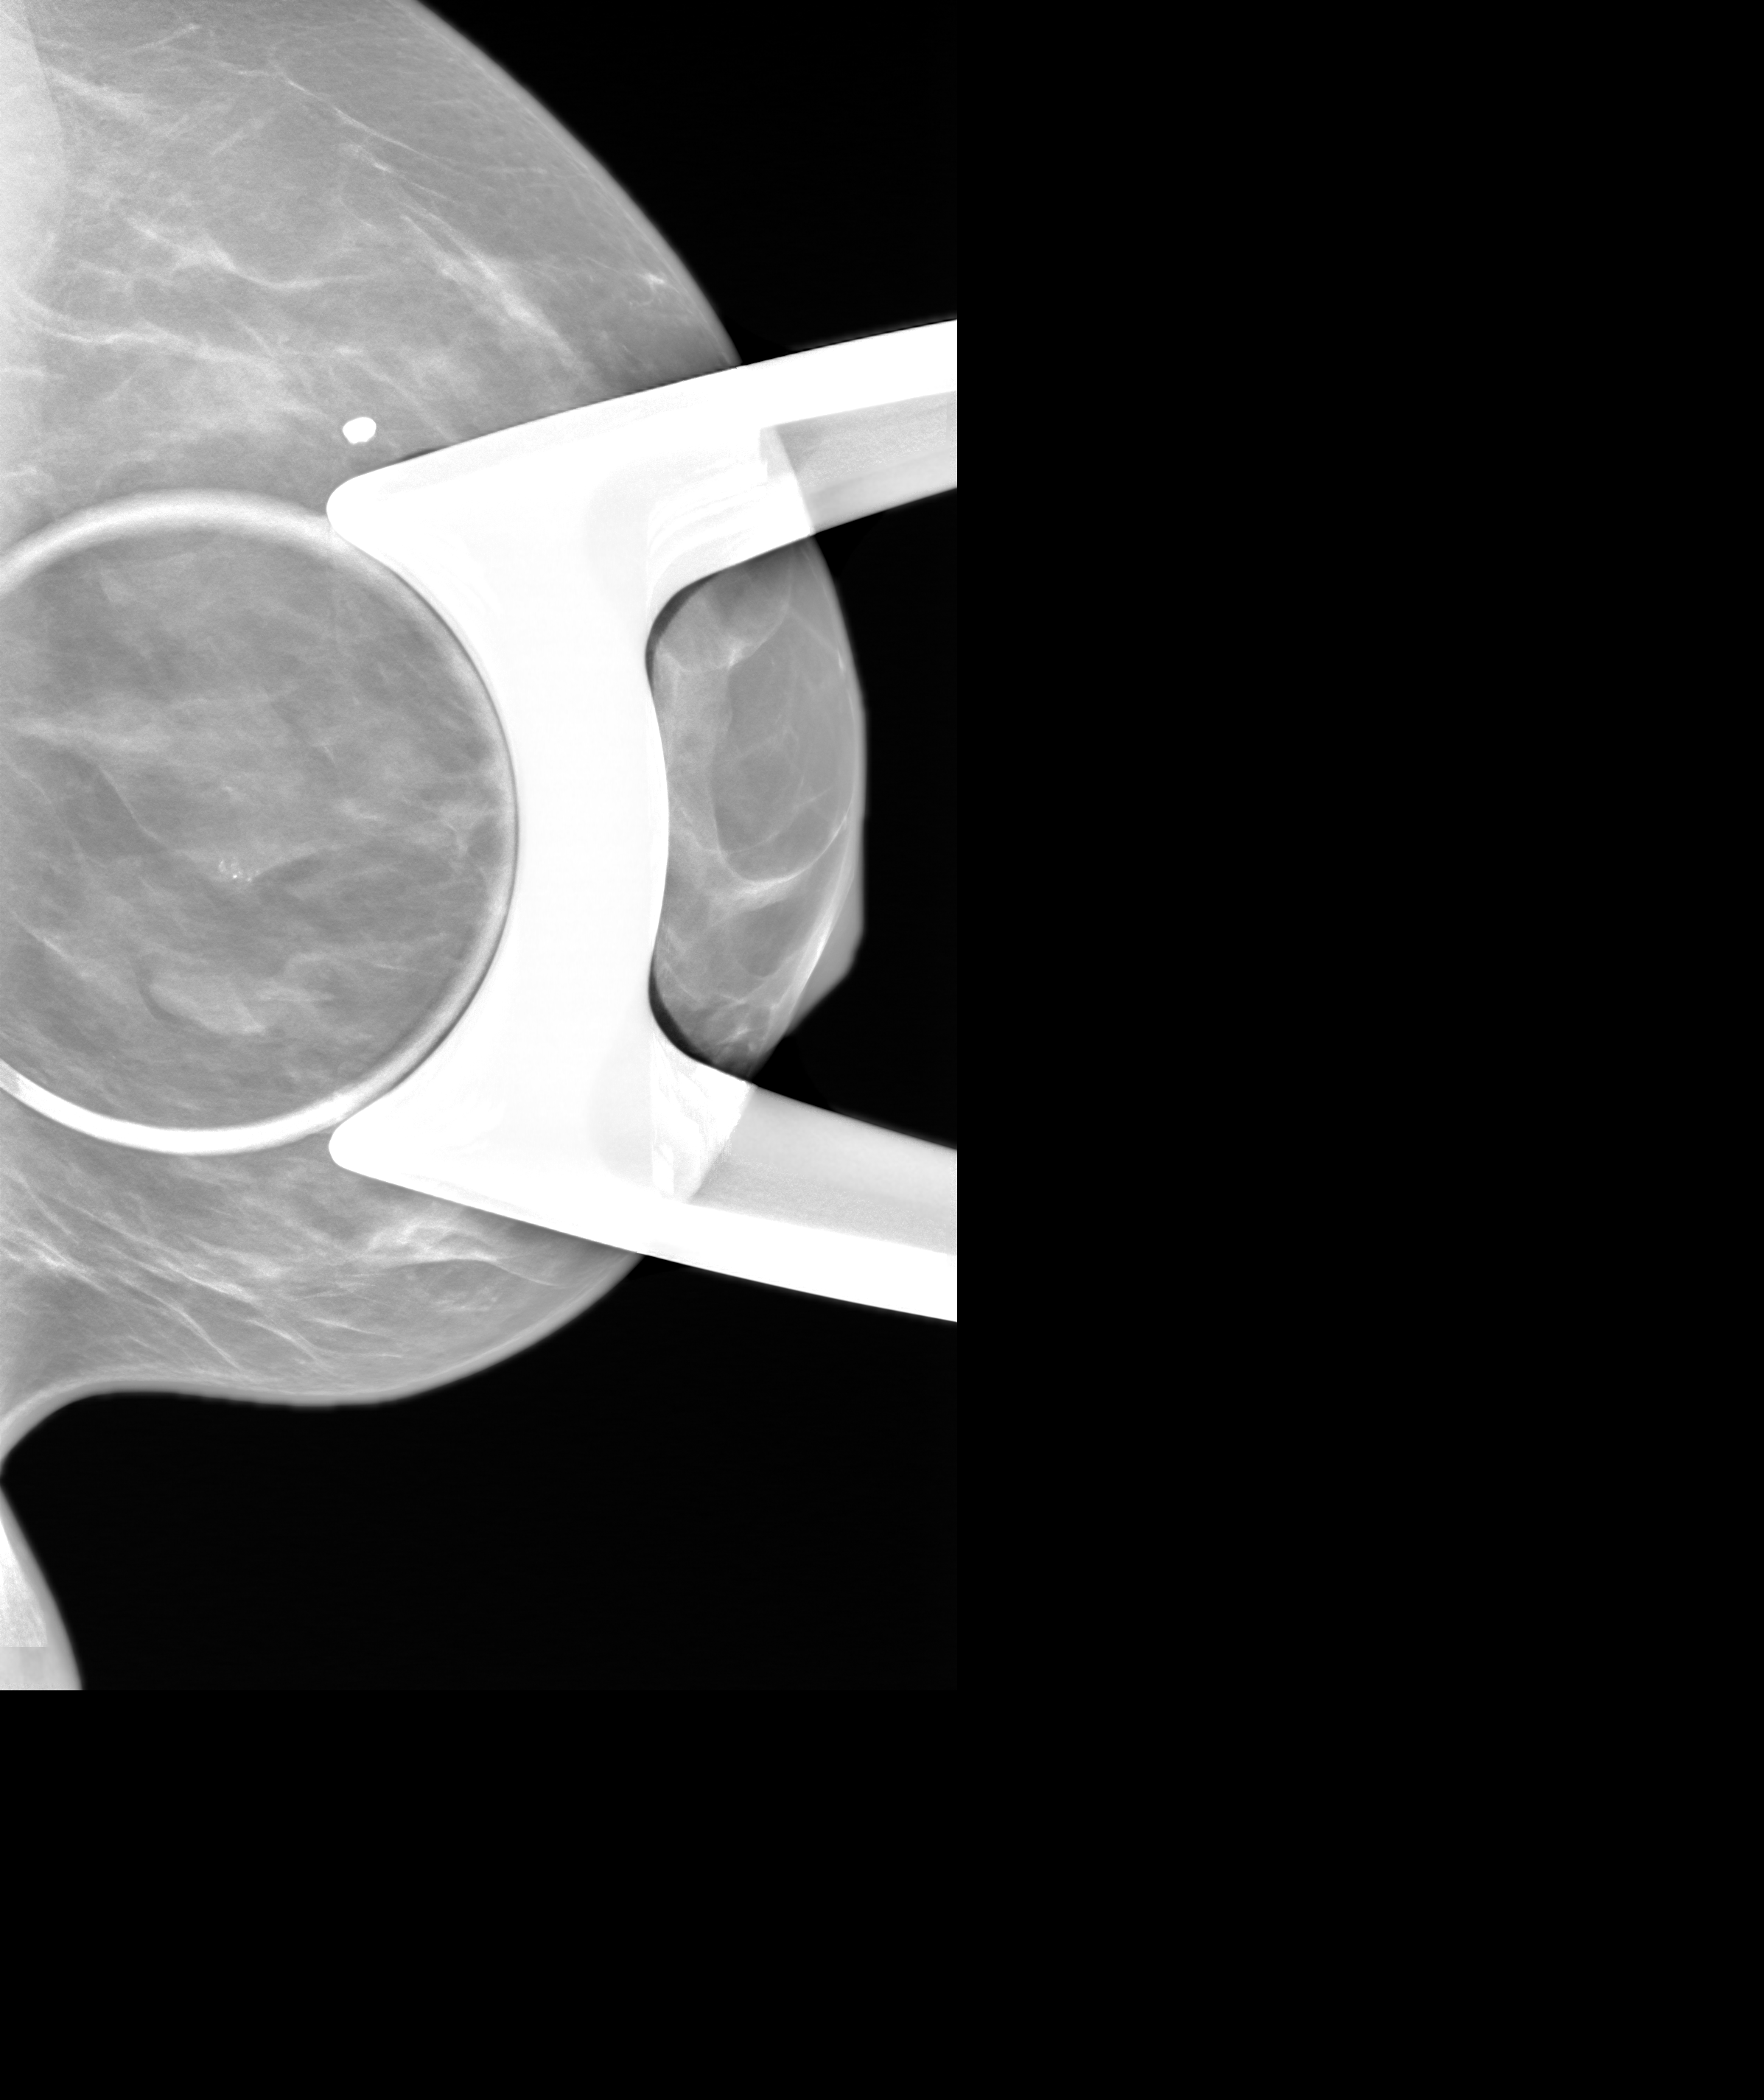
Additional (diagnostic) view; system: SenoIris_1SP2(440). Female patient, age 52 years.
Image type: synthesized 2-D view from tomosynthesis. Breast: left. Projection: LM view, spot compression.